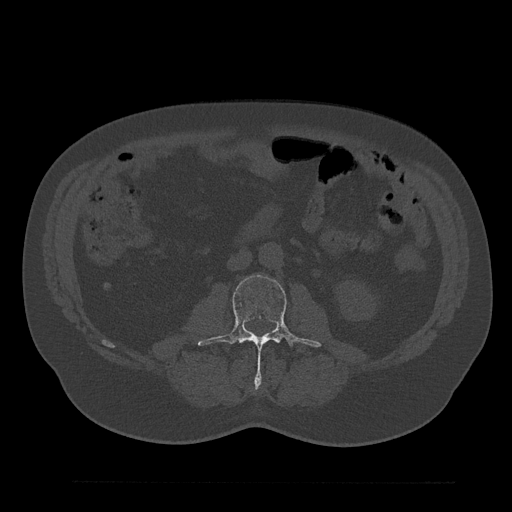
CT including the spine, one axial slice; position 37 of 797 along the scan axis; bone window (W 1800 / L 400 HU); 0.5 mm slice thickness; 512 × 512 image matrix. Patient: male, 61 years. Case-level facts recorded for this patient, not image findings: primary cancer: prostate.
Structures marked on this image (semi-automatically segmented with operator editing):
- L3 vertebra: bounding box [x1, y1, x2, y2] px = [198, 274, 321, 385]